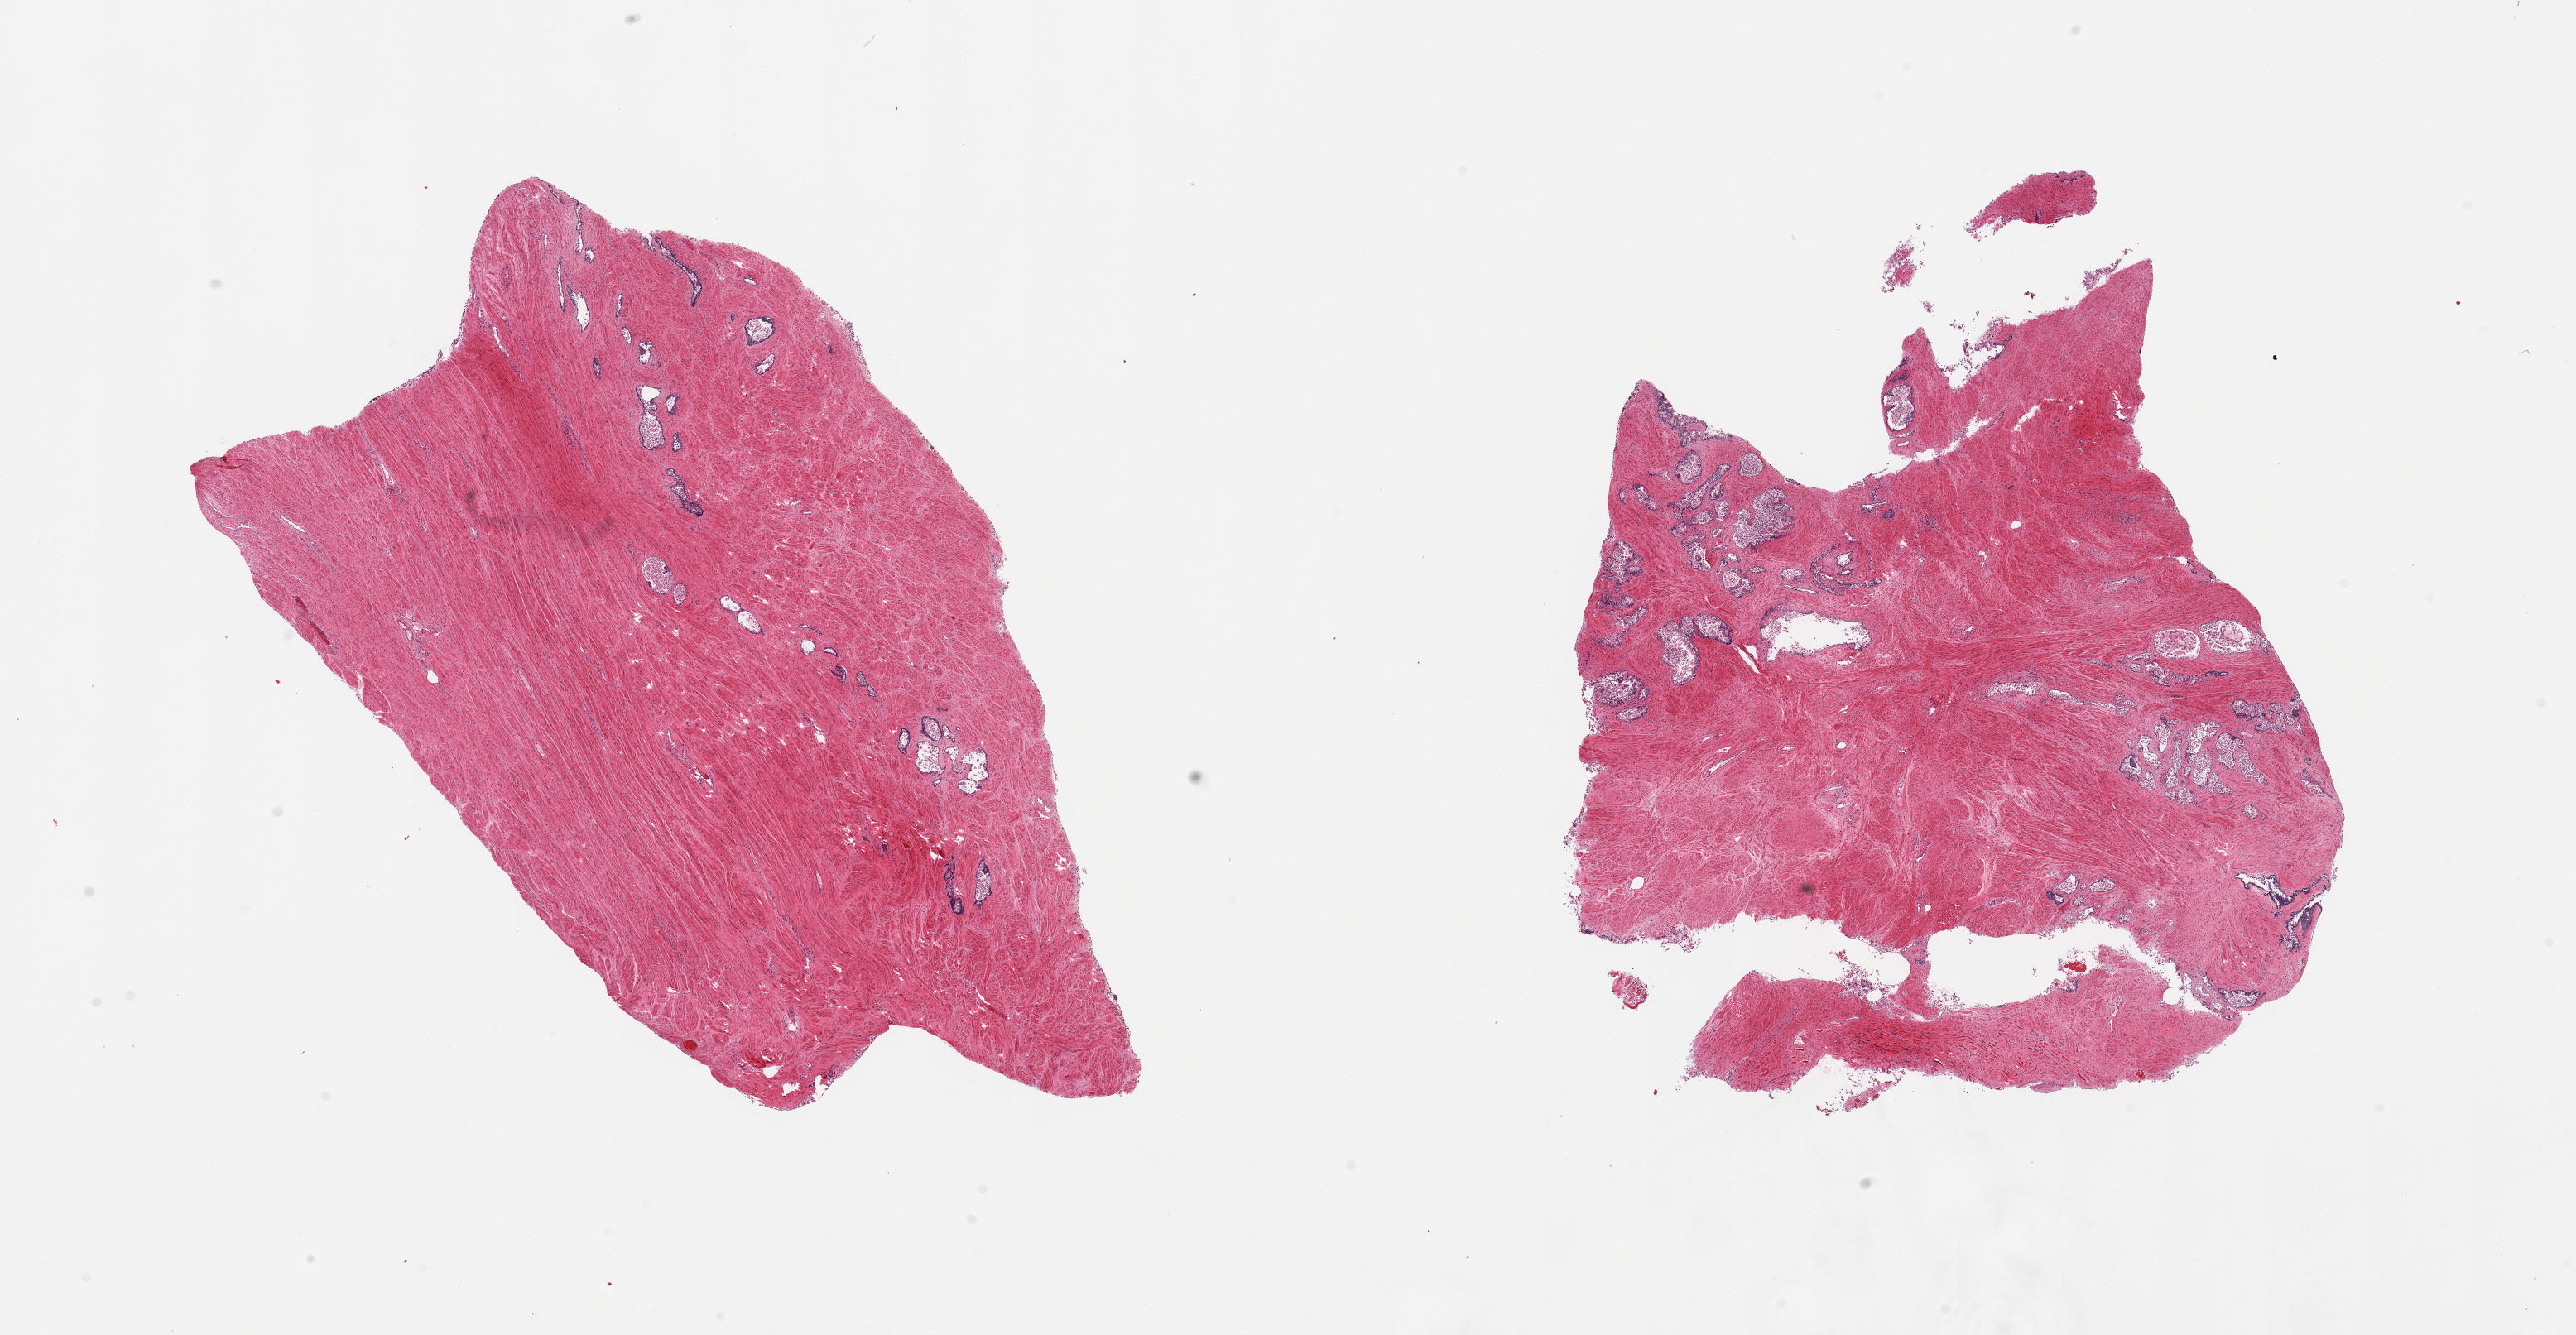
Hematoxylin and eosin (H&E) whole-slide image, low-resolution overview of the scanned area, about 24.6 x 12.8 mm (acquisition: 20x scan), PAXgene-fixed, paraffin-embedded tissue, sampled site (target tissue): prostate, tissue donor sample. Male donor.
Review note (as recorded): 2 pieces; predominantly stroma with some glands with sloughing epithelium, small component of skeletal muscle in one piece.